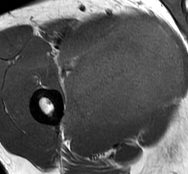
MRI of an extremity soft-tissue mass, one axial slice; position 45 of 93 along the scan axis; MR volume resampled by the dataset authors to the PET/CT grid (not the native acquisition matrix); 188 × 174 image matrix, field of view 184 × 170 mm. Male patient. From the clinical record (not read from this slice): histological type: undifferentiated - pleiomorphic; grade: high; site of the primary tumour: right thigh.
Outlined on this slice (expert contour drawn on MRI and transferred to this co-registered scan by the dataset authors):
- gross tumour volume including surrounding oedema: bounding box [x1, y1, x2, y2] px = [59, 16, 185, 130]
- gross tumour volume (mass): [70, 19, 185, 125]